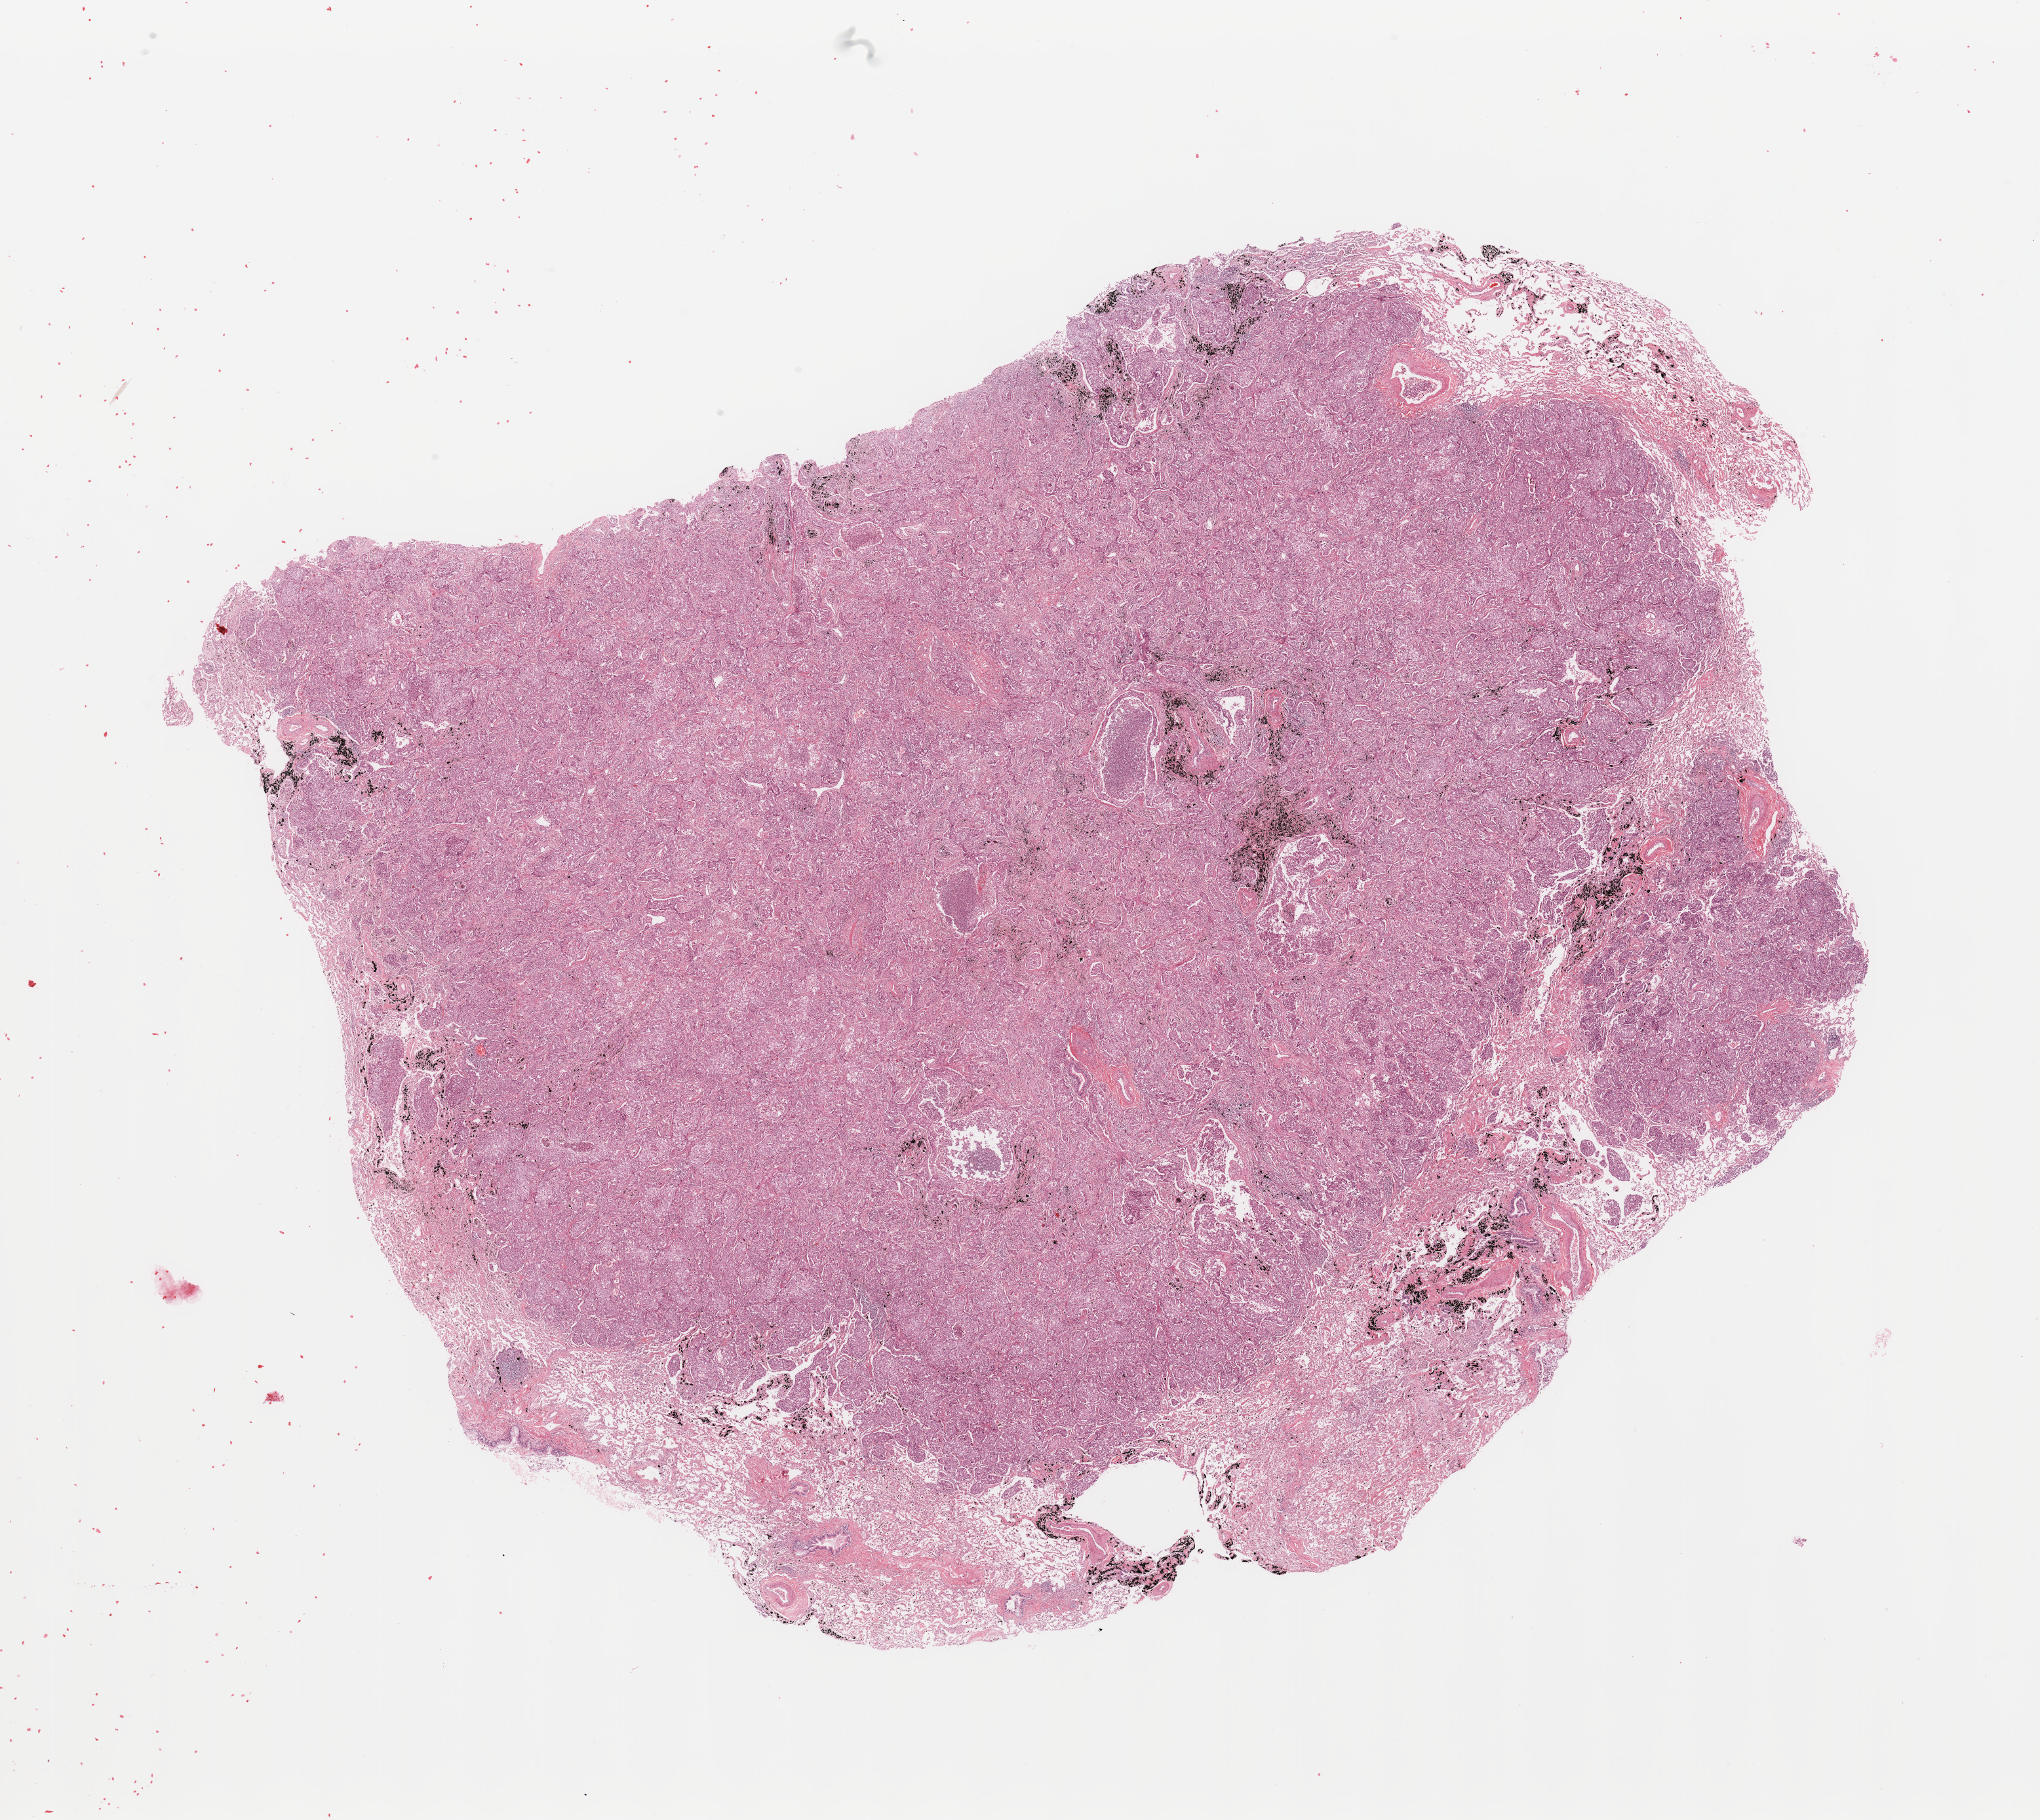
H&E-stained whole-slide image — low-resolution overview of the scanned area, about 24.6 x 22.0 mm. Tumour tissue sample, lung. Patient: male, age 54 years. Histologic grade: G3 (poorly differentiated).
AJCC pathologic stage: IB. Diagnosis: Adenocarcinoma, NOS.